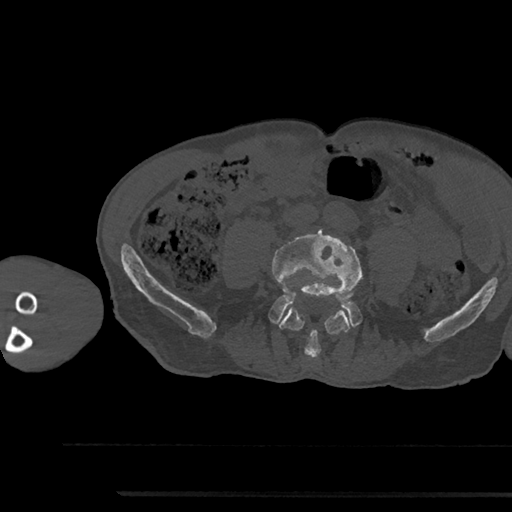
CT including the spine, one axial slice; position 386 of 797 along the scan axis; reconstruction kernel Br40s/3; bone window (W 1800 / L 400 HU); 0.5 mm slice thickness; 512 × 512 image matrix, field of view 367 × 367 mm. Male patient, age 79 years. Case-level facts recorded for this patient, not image findings: primary cancer: prostate.
Annotated regions visible in this slice (semi-automatic segmentation, software-assisted and operator-edited):
- L4 vertebra: bounding box (x1, y1, x2, y2) in pixels: (272, 229, 362, 358)
- L5 vertebra: (270, 295, 361, 326)